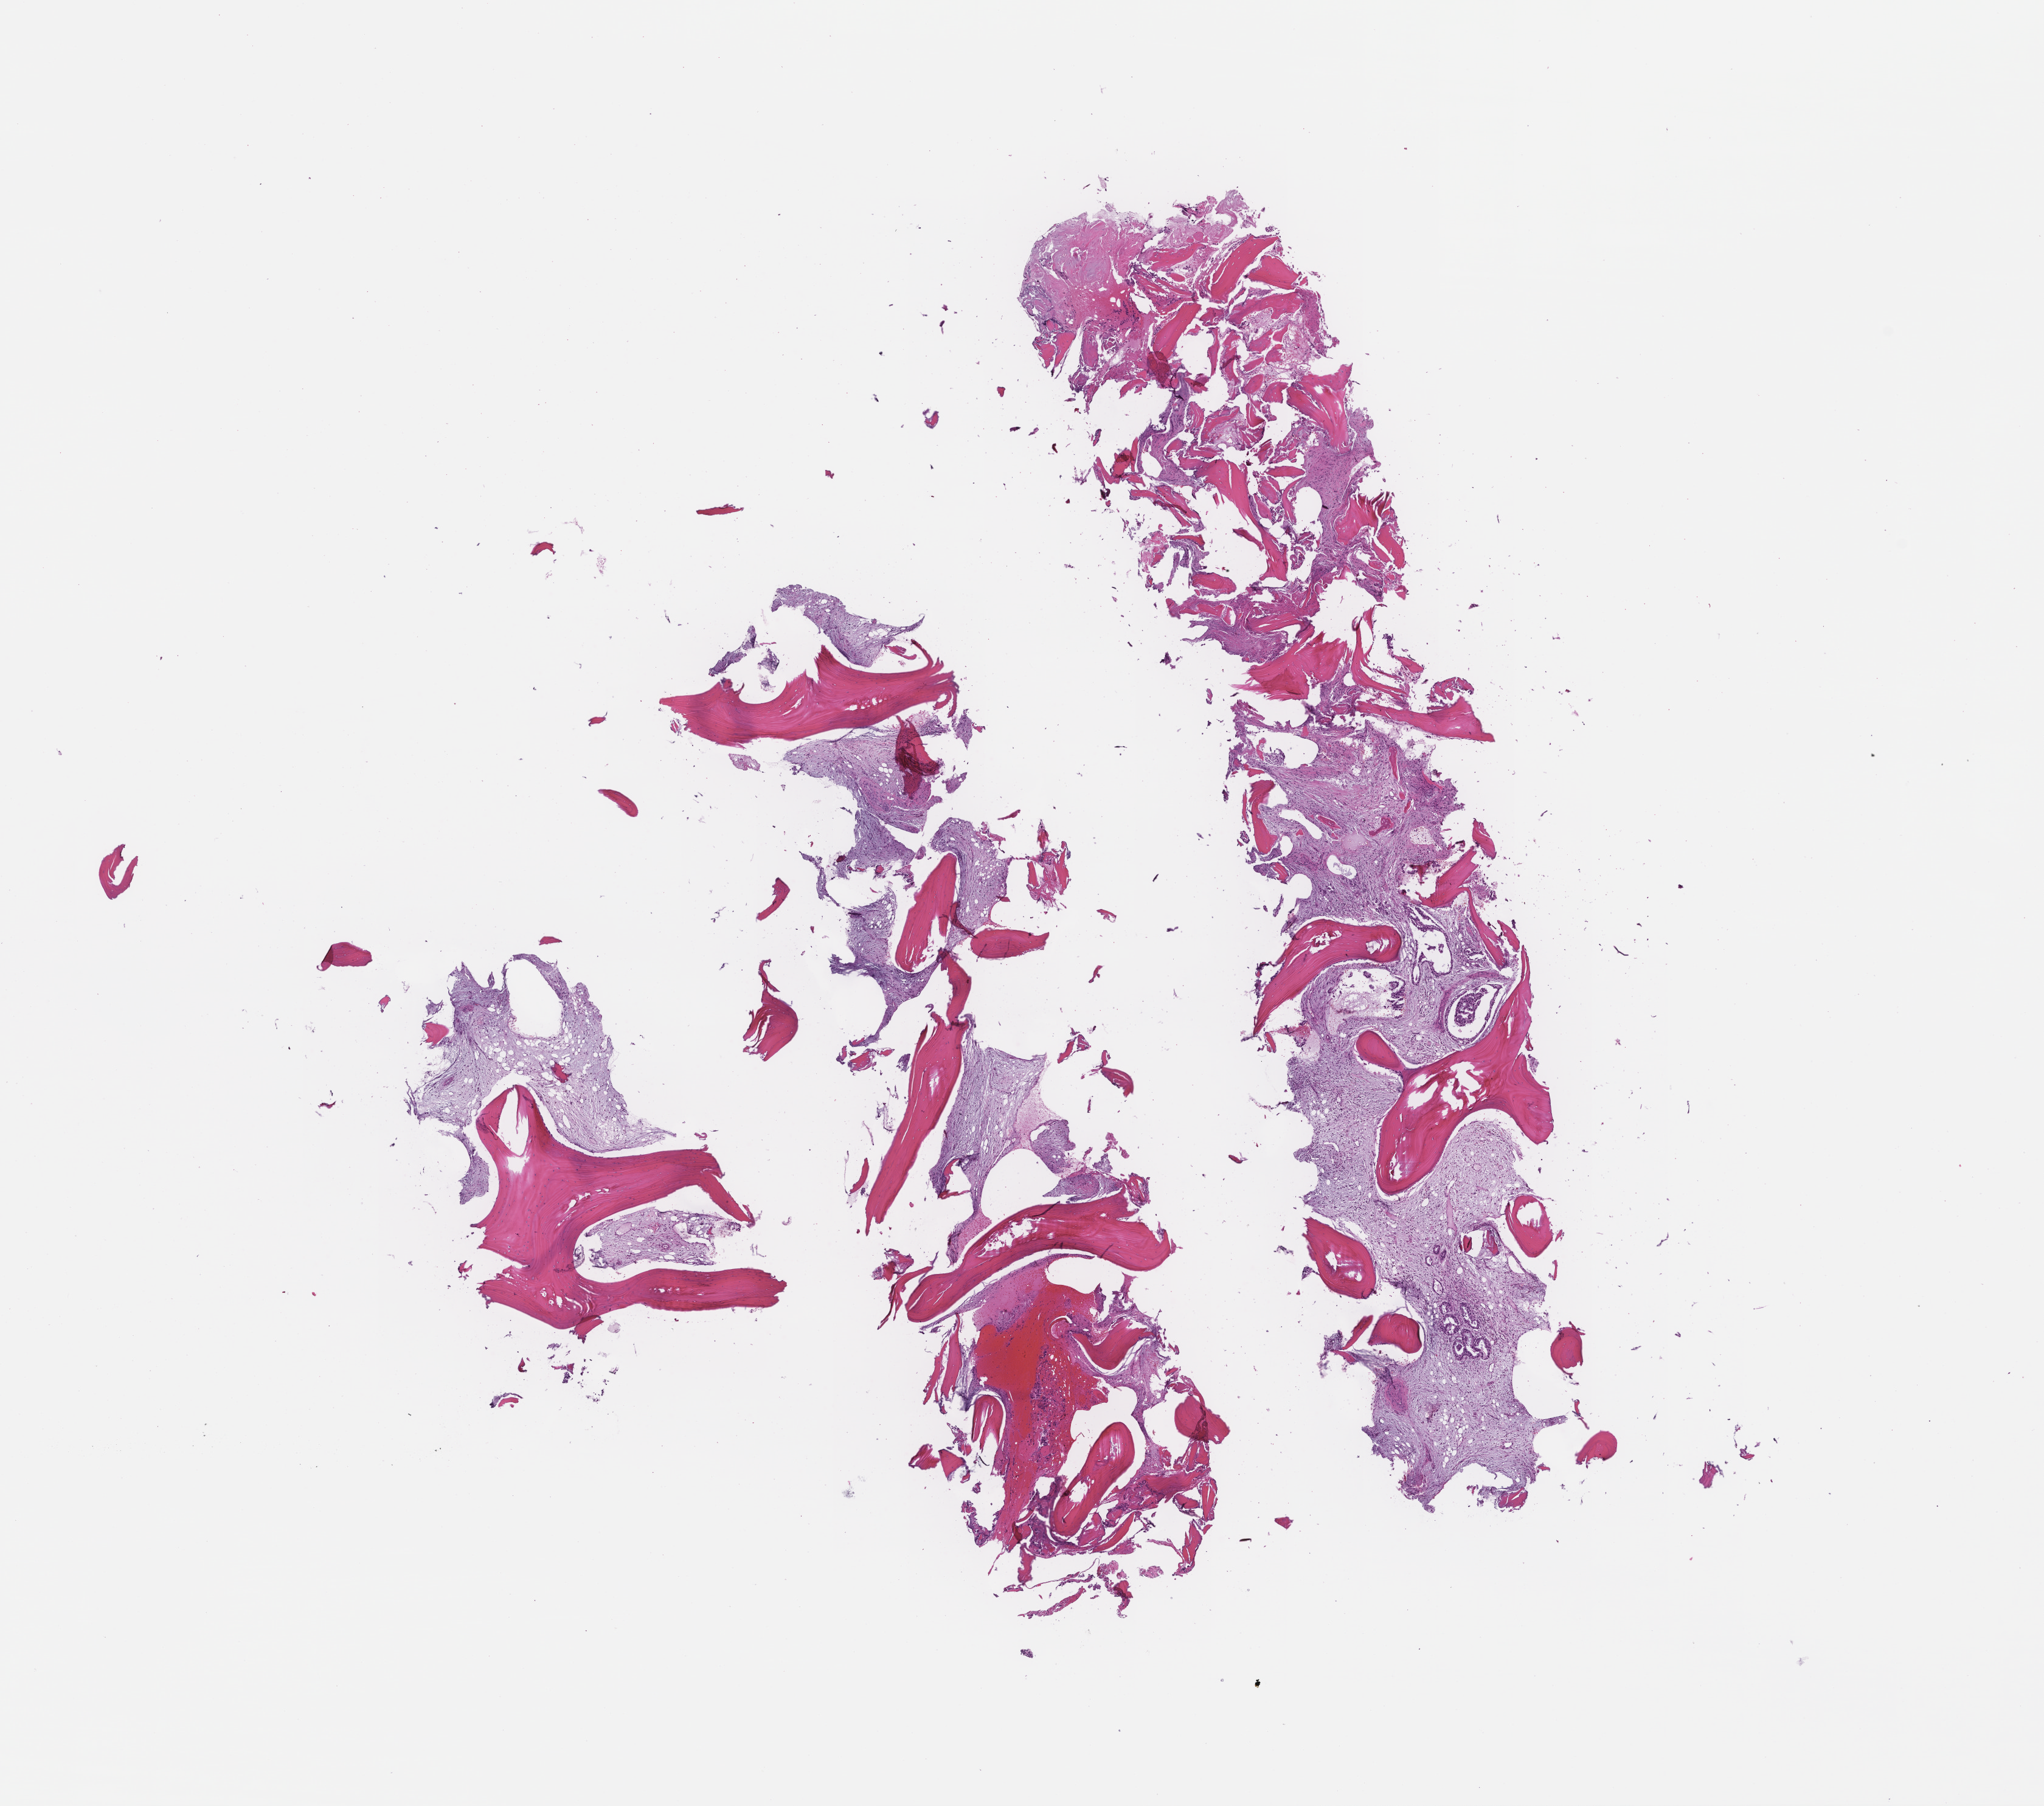
Haematoxylin and eosin whole-slide image — low-resolution overview of the scanned area, about 13.6 x 12.0 mm. FFPE section. Archival tissue. Patient: female.
This section: metastatic tumor tissue. Primary diagnosis of the patient: Non-Small Cell Lung Carcinoma.